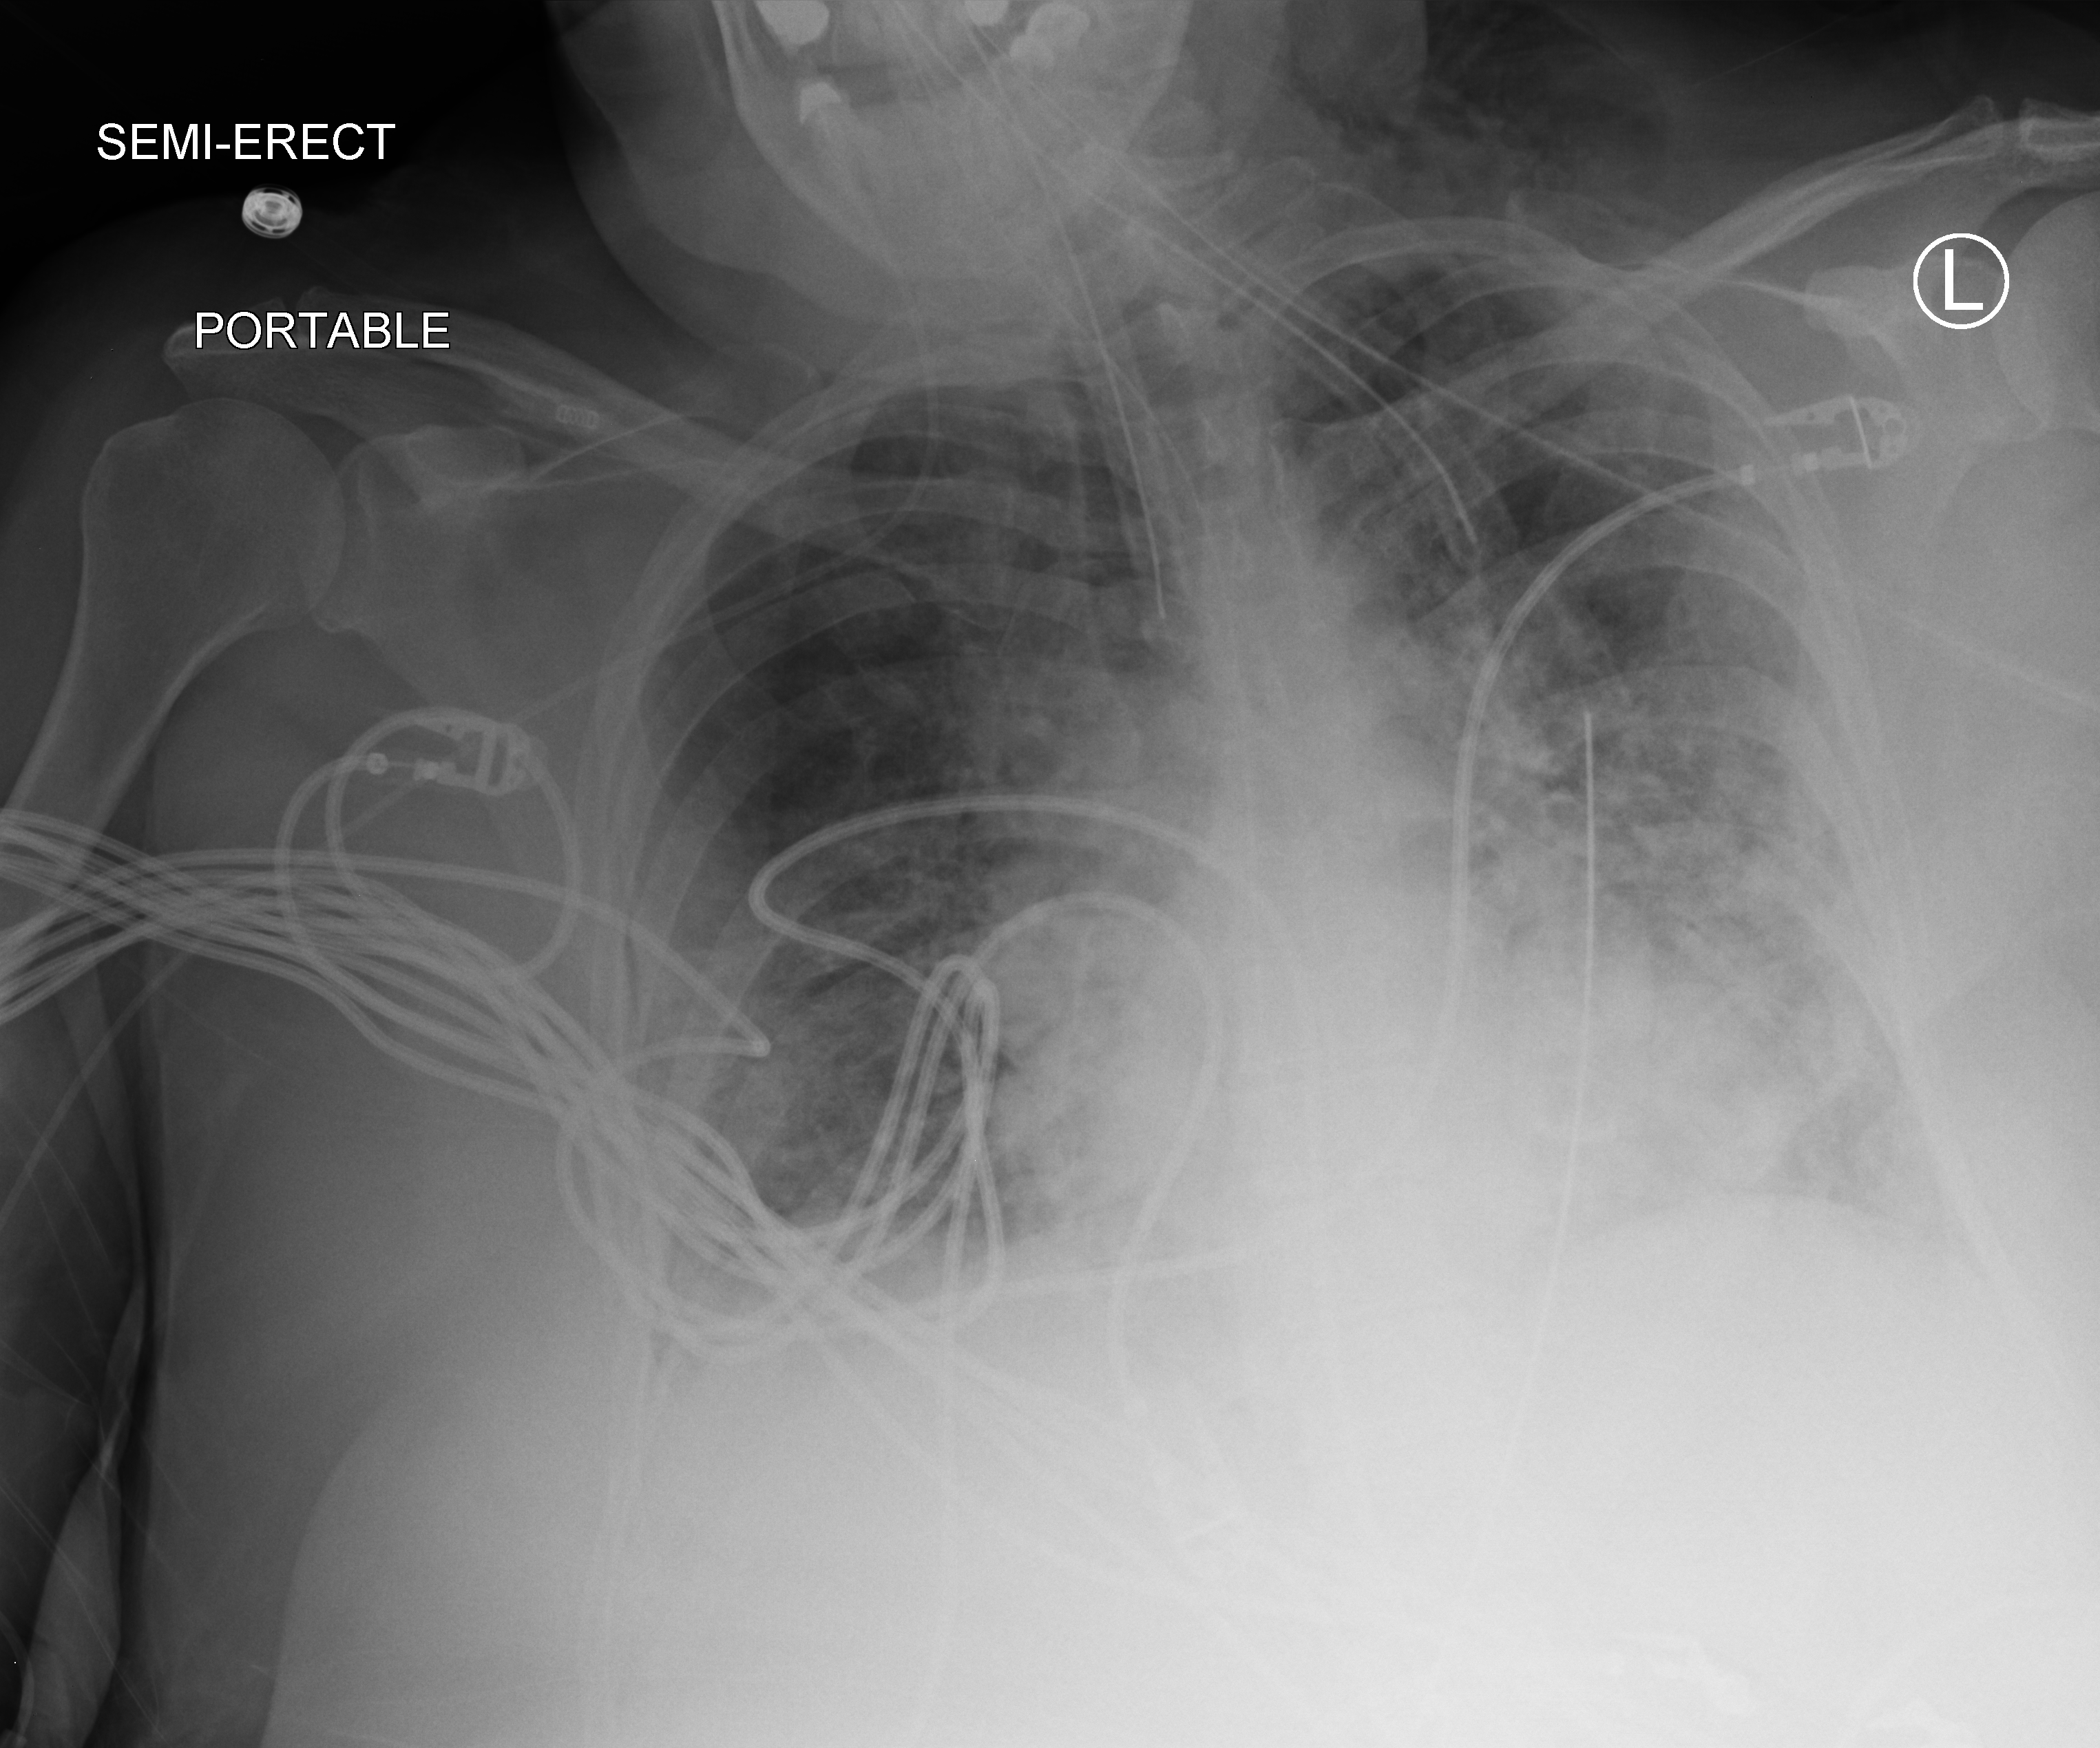
Chest X-ray (portable). Patient hospitalised with COVID-19; female, aged 60–74 years.
Hospital-stay facts (about this admission, not read from this image; timing relative to this image not recorded):
- diabetes (admission record): no